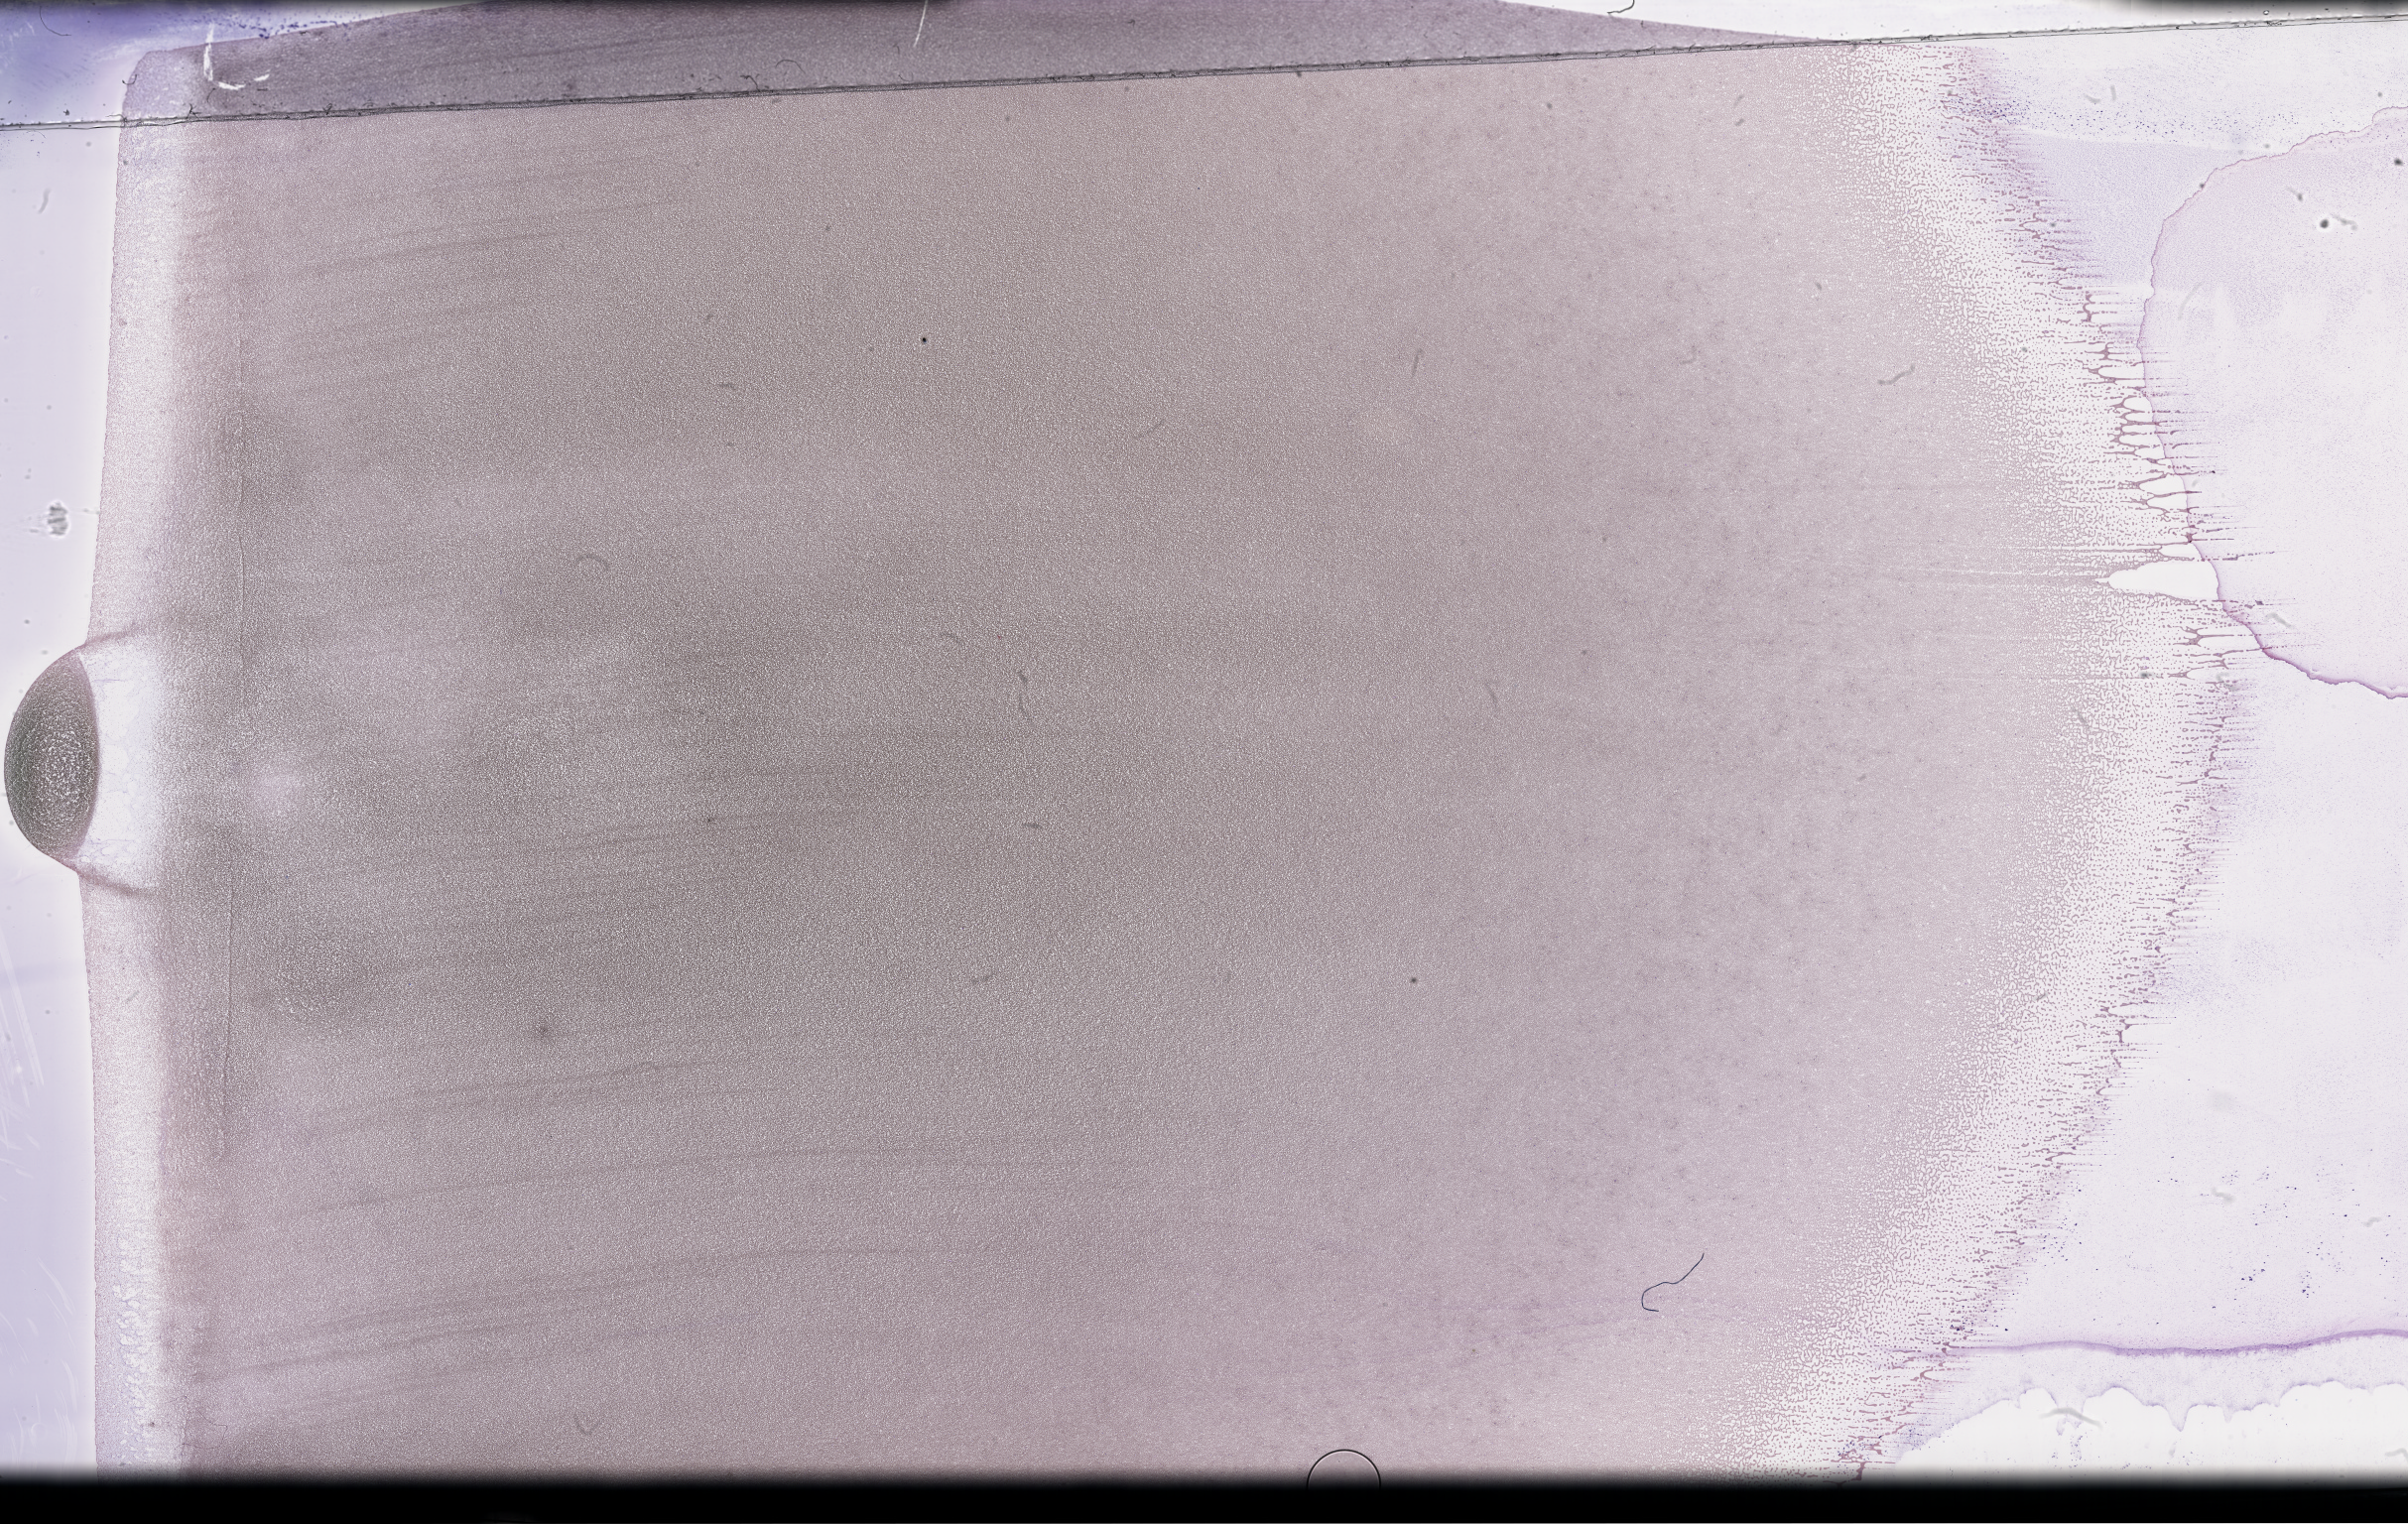
Wright–Giemsa-stained whole blood smear, whole-slide image, whole scanned area (about 39.2 x 24.8 mm) shown as a low-resolution overview. Patient sex: male.
From a patient with: Plasma Cell Myeloma.